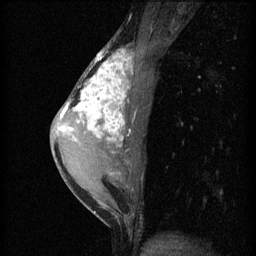
Breast MRI (dynamic contrast-enhanced), one sagittal slice; position 29 of 60 along the scan axis; 3 images stored at this slice position (order not interpretable as contrast timing); 1.5 T; TE 4.2 ms, TR 11 ms; 2 mm slice thickness; 256 × 256 image matrix. Female patient, age 40 years.
Outlined on this slice (semi-automatic segmentation, software-assisted and operator-edited):
- analysis volume of interest (the breast-tissue region the enhancement analysis was run in; not a lesion): bounding box (x1, y1, x2, y2) in pixels: (55, 42, 141, 203)
- tumour enhancement mask (voxels above the 70 % enhancement threshold inside the analysis volume of interest): (59, 50, 133, 147)